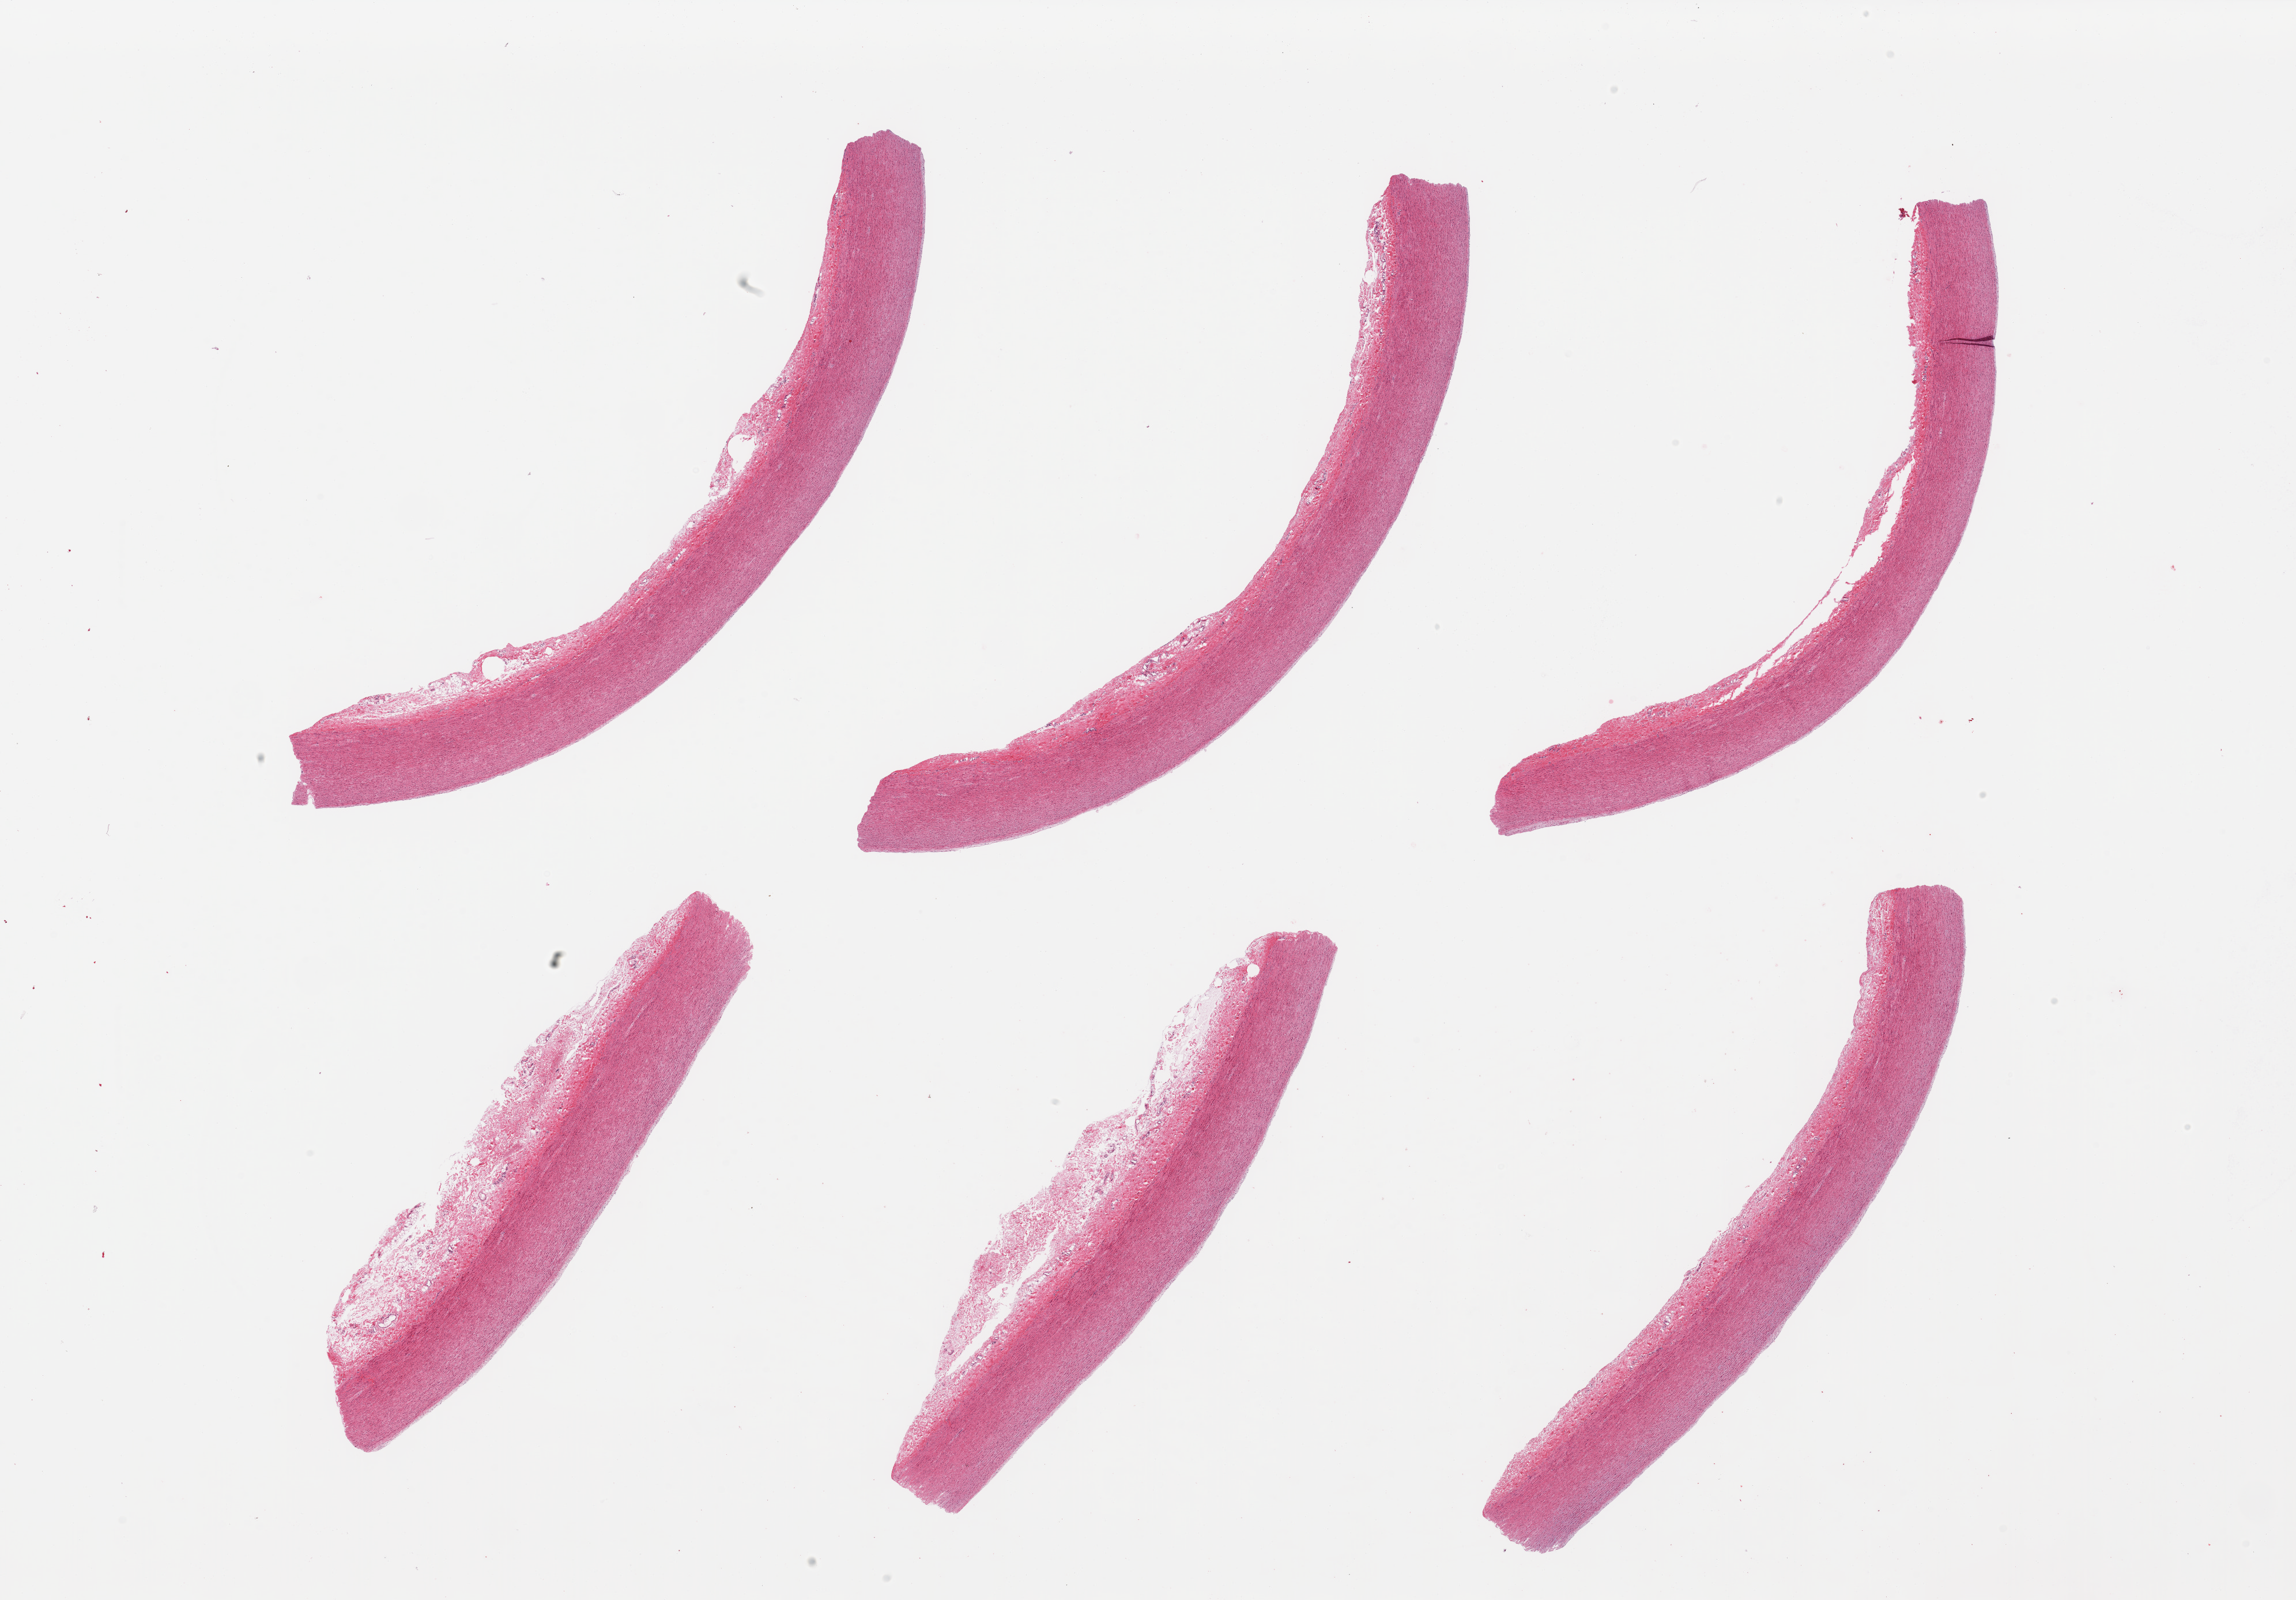
Digitized hematoxylin and eosin (H&E)-stained section — shown as a low-resolution overview of the whole scanned area (about 31.5 x 22.0 mm, slide scanned at 20x). PAXgene-fixed, paraffin-embedded tissue. Sampled site (target tissue): aorta. Tissue donor sample. Female donor.
• pathologist's review note for this sample: 6 pieces